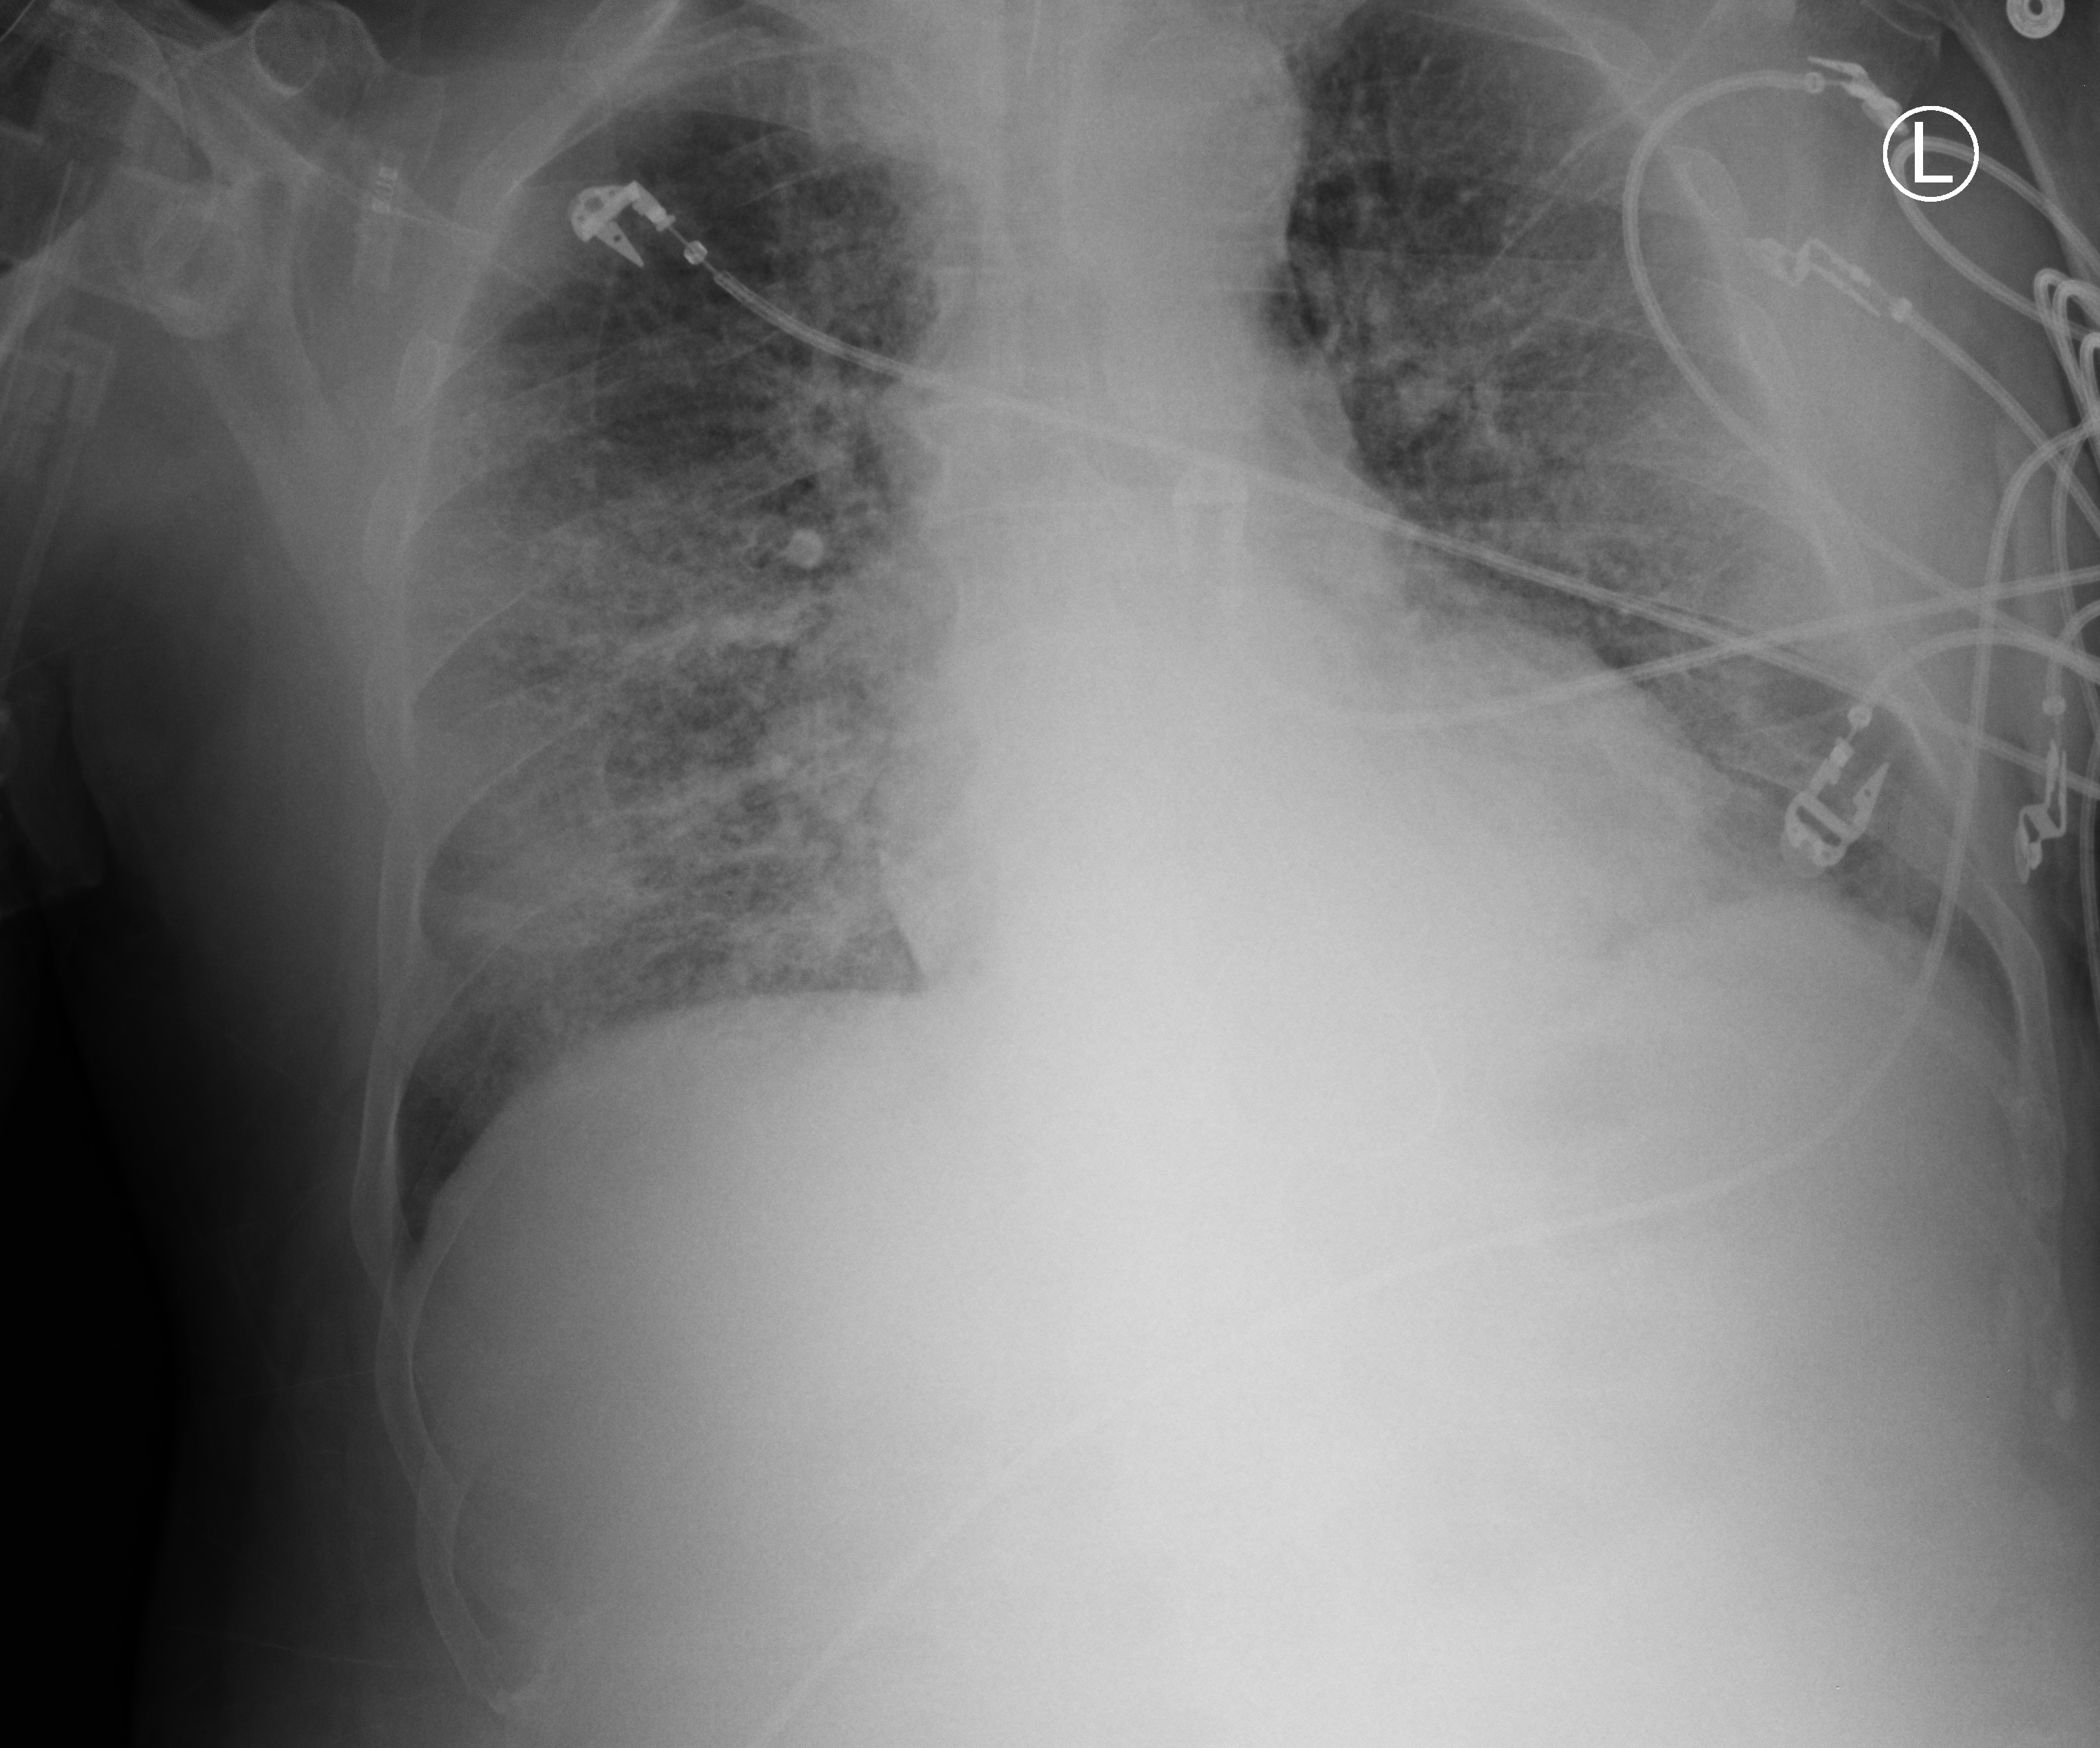
Bedside chest radiograph (computed radiography). Patient hospitalised with COVID-19; male, aged 75–90 years.
Hospital-stay facts (about this admission, not read from this image; timing relative to this image not recorded): mechanically ventilated during this hospital stay: yes; admitted to intensive care during this hospital stay: yes.